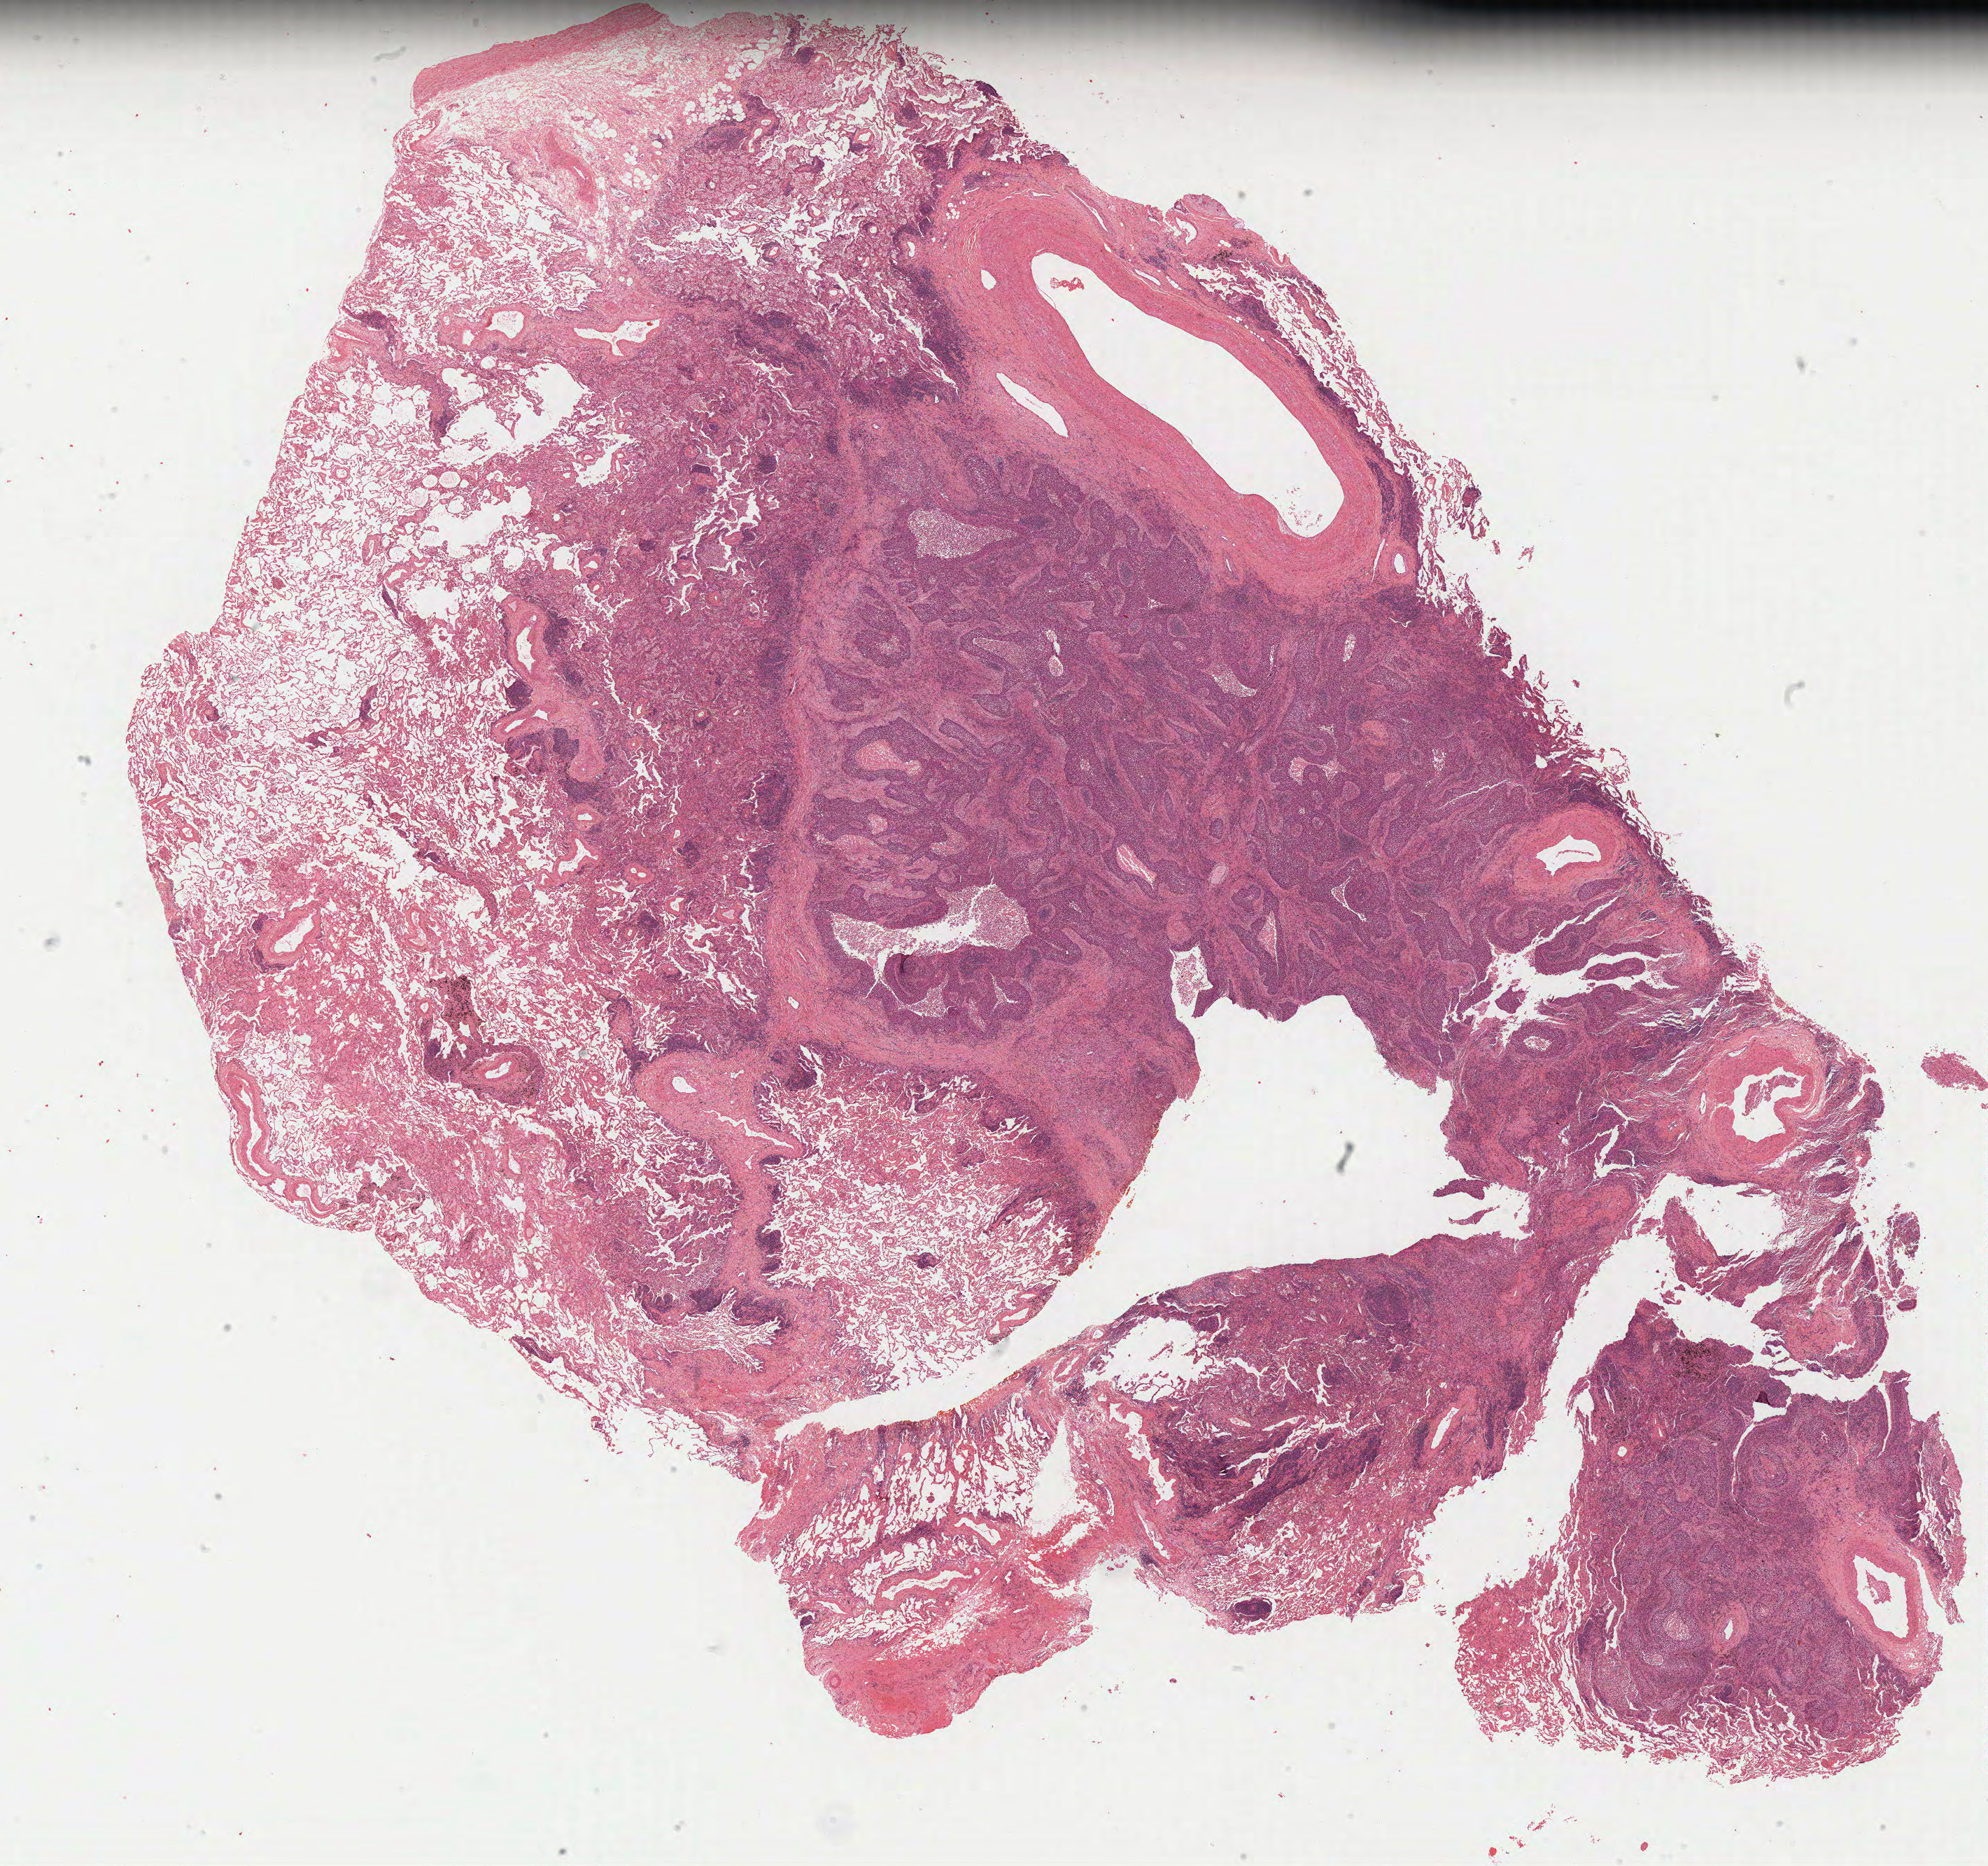
Hematoxylin and eosin (H&E) stained whole-slide image, whole scanned area (about 22.9 x 21.5 mm, acquisition: 40x scan) shown as a low-resolution overview, FFPE section, lung, primary tumour sample. Patient: male, age at initial diagnosis 74 years.
Histologic diagnosis: Squamous cell carcinoma, NOS (lower lobe, lung). AJCC pathologic stage: IA. Laterality: left.